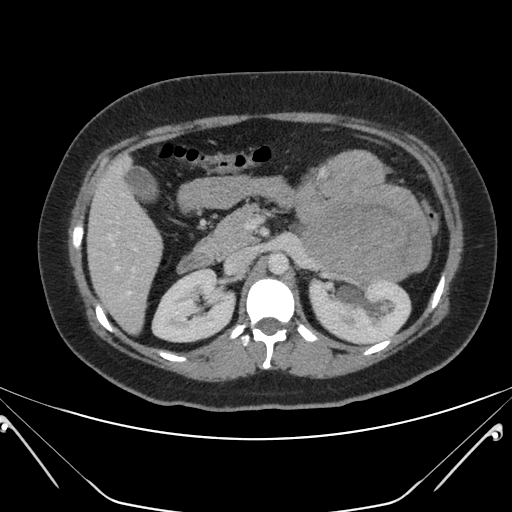
Contrast-enhanced abdominal CT, one axial slice. Slice 119 of 168 in the series (ordered by position). 120 kVp. Intravenous contrast given. Soft-tissue window (W 400 / L 40 HU). 3 mm slice thickness. 512 × 512 image matrix, field of view 394 × 394 mm. Patient: female, 26 years. Case-level facts recorded for this patient, not image findings: diagnosis: adrenocortical carcinoma; tumour side: left adrenal; tumour size at pathology: 28 cm; Ki-67 index: 20 %; stage (as recorded): 2.
Structures marked on this image (semi-automatic segmentation, software-assisted and operator-edited):
- mass: box from (x=296, y=152) to (x=430, y=280) px